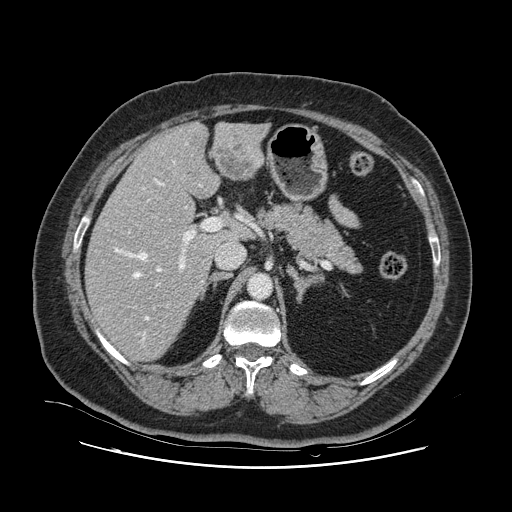
Contrast-enhanced abdominal CT, one axial slice; position 65 of 132 along the scan axis; 120 kVp; intravenous contrast given; soft-tissue window (W 400 / L 40 HU); 2.5 mm slice thickness; 512 × 512 image matrix, field of view 391 × 391 mm. Female patient, age 73 years. Case-level facts recorded for this patient, not image findings: diagnosis: colorectal cancer liver metastases, imaged before liver resection; multiple liver metastases: no; largest metastasis: 7 cm; chemotherapy before resection: yes.
Outlined on this slice (manually delineated by an expert):
- hepatic veins: bounding box [x1, y1, x2, y2] px = [114, 161, 202, 342]
- liver: [86, 124, 265, 360]
- planned liver remnant (the part of the liver to remain after resection): [86, 150, 224, 360]
- portal vein (with intrahepatic branches): [129, 218, 222, 270]
- liver metastasis: [218, 149, 258, 177]